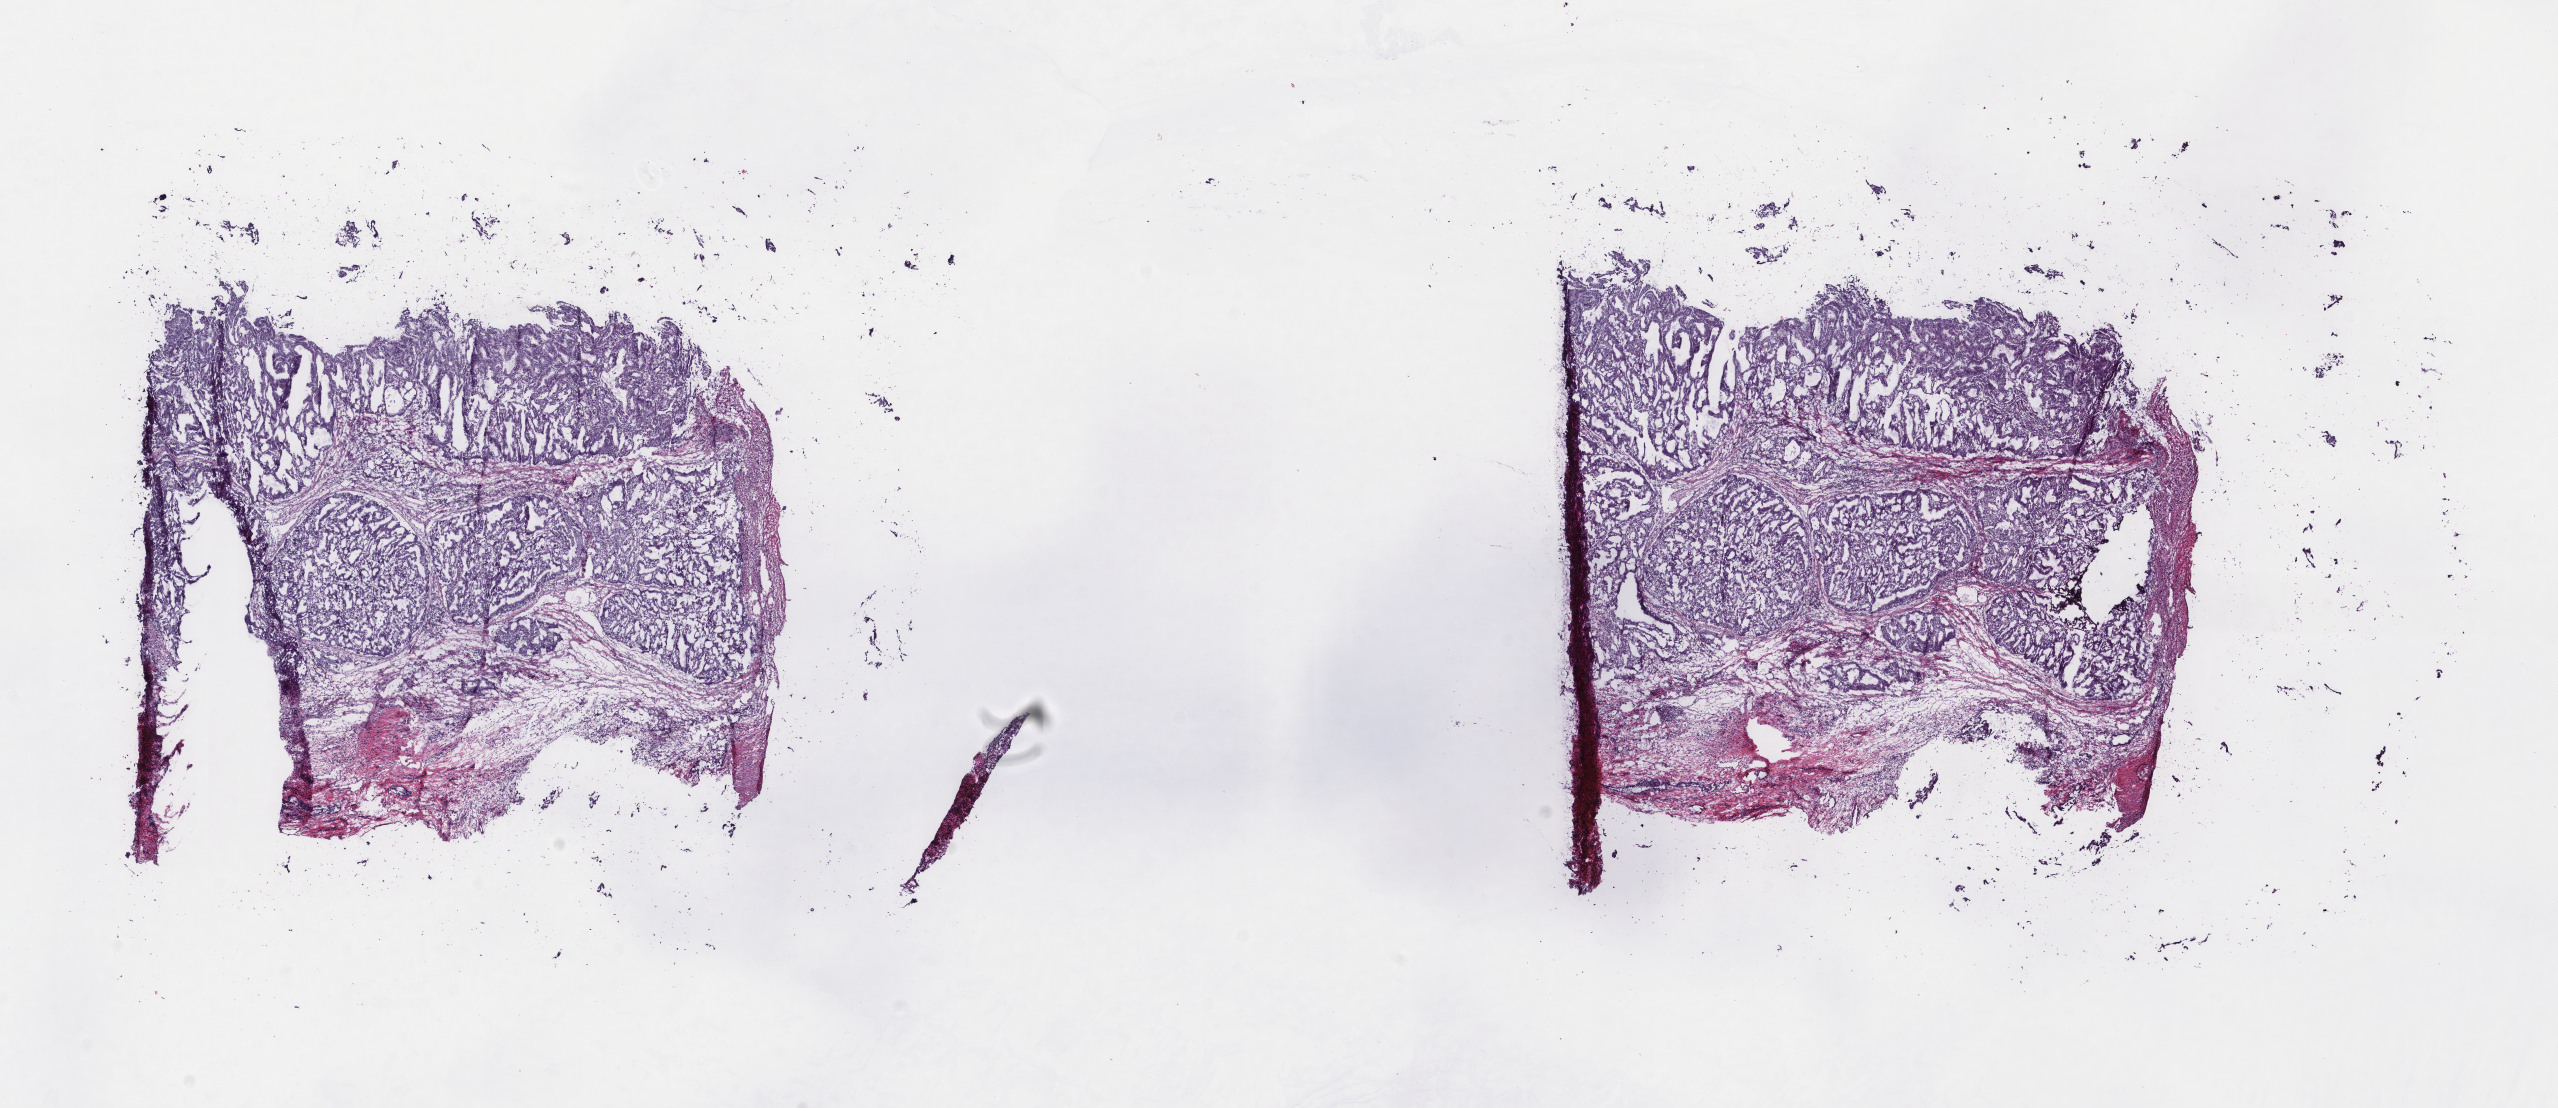
Whole-slide histology image, H&E — whole scanned area (about 20.3 x 8.8 mm, acquisition: 40x scan) shown as a low-resolution overview; frozen section from the top of the tissue portion; sample: primary tumour, uterus. Patient: female, age at initial diagnosis 61 years. Histologic grade: G2 (moderately differentiated). Slide review estimates, as recorded: tumour cells 80%, tumour nuclei 70%, normal cells 20%, stromal cells 0%, necrosis 0%. Infiltration values recorded for this section: lymphocyte infiltration 0%, monocyte infiltration 0%, neutrophil infiltration 0%.
Diagnosis: Endometrioid adenocarcinoma, NOS (endometrium). FIGO stage: IIIA.